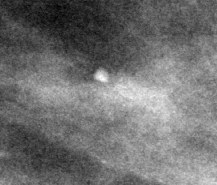
Cropped region of a digitized screen-film mammogram centred on a radiologist-marked abnormality, left breast, MLO view, BI-RADS breast density category 2 (scale 1–4).
Finding: calcifications, morphology punctate; BI-RADS assessment category 2; benign; no additional work-up was recommended (benign without callback).